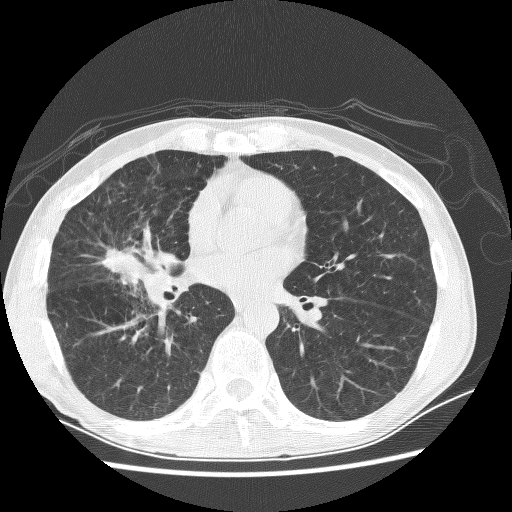
Low-dose screening chest CT, axial slice. First (baseline) screen. Lung window (W 1500 / L -600 HU). 2.5 mm slice thickness. 512 × 512 image matrix. Male participant, aged 67 years at enrolment. Current smoker at enrolment.
- Lesion marked by an expert reader, bounding box (x1, y1, x2, y2) in pixels: (77, 224, 173, 297).
- Screening reader's record for this exam (one nodule recorded; not confirmed to be the boxed lesion): non-calcified nodule or mass ≥4 mm, right middle lobe, 28 × 18 mm, spiculated (stellate) margins, soft tissue attenuation.
- Official screen result: positive, change unspecified: nodule(s) >= 4 mm or enlarging nodule(s), mass(es), or other non-specific abnormalities suspicious for lung cancer.
- Participant outcome: lung cancer diagnosed 69 days after this screen — adenocarcinoma, NOS, right middle lobe, stage IV (AJCC 6th edition), 60 mm at pathology.